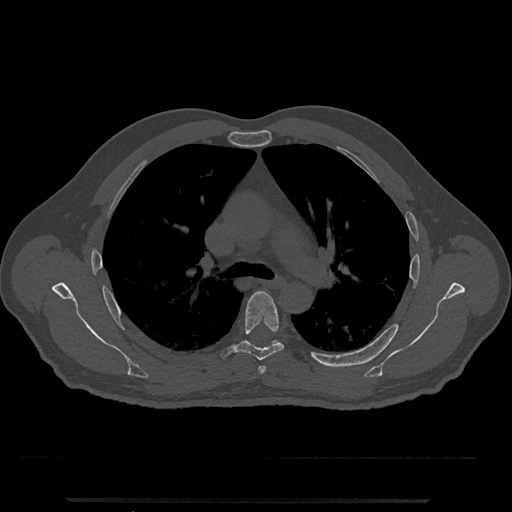
CT including the spine, one axial slice; slice 791 of 797 in the series (ordered by position); reconstruction kernel Br40s/3; 120 kVp; bone window (W 1800 / L 400 HU); 0.5 mm slice thickness; 512 × 512 image matrix. Patient: male, 63 years. Case-level facts recorded for this patient, not image findings: primary cancer: prostate.
Structures marked on this image (semi-automatically segmented with operator editing):
- T5 vertebra: bounding box [x1, y1, x2, y2] px = [221, 291, 284, 361]
- T6 vertebra: [272, 340, 280, 345]